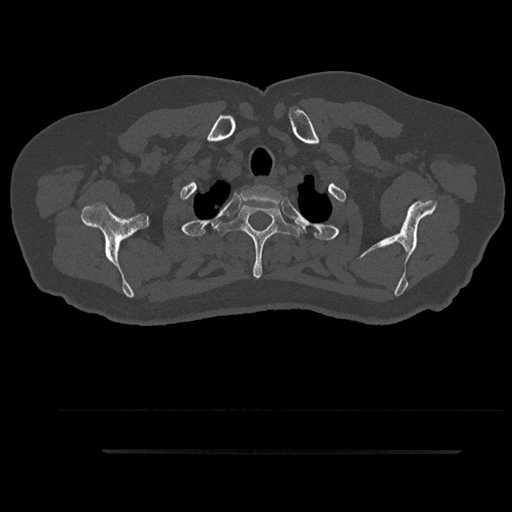
CT including the spine, one axial slice. Position 766 of 797 along the scan axis. Reconstruction kernel Br40s/3. 120 kVp. Bone window (W 1800 / L 400 HU). 0.5 mm slice thickness. 512 × 512 image matrix. Patient: male, 63 years. Case-level facts recorded for this patient, not image findings: primary cancer: renal; vertebrae with lytic lesions (as recorded): T8.
Structures marked on this image (semi-automatically segmented with operator editing):
- T1 vertebra: bounding box (x1, y1, x2, y2) in pixels: (238, 185, 283, 217)
- T2 vertebra: (214, 205, 303, 279)